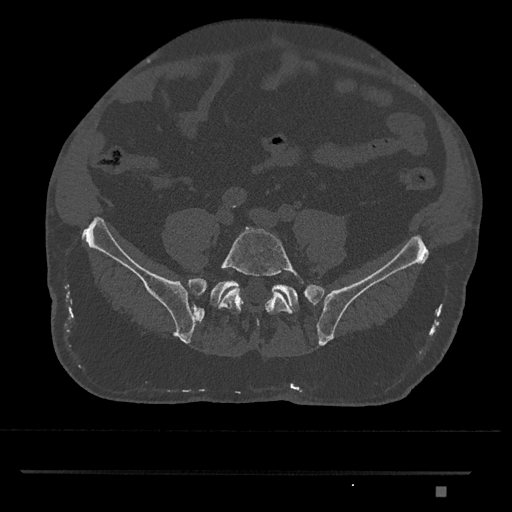
CT including the spine, one axial slice; slice 542 of 1134 in the series (ordered by position); 120 kVp; bone window (W 1800 / L 400 HU); 0.5 mm slice thickness; 512 × 512 image matrix. Male patient, age 65 years. From the clinical record (not read from this slice): primary cancer: prostate.
Outlined on this slice (semi-automatically segmented with operator editing):
- L5 vertebra: bounding box (x1, y1, x2, y2) in pixels: (218, 226, 305, 328)